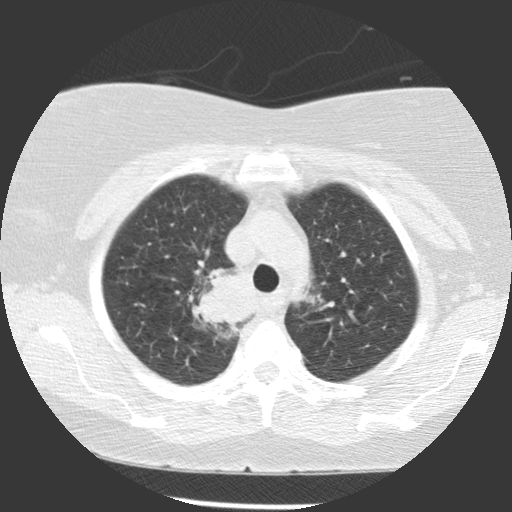
Axial slice from a low-dose chest CT screening exam; first (baseline) screen; lung window (W 1500 / L -600 HU); 2.5 mm slice thickness; standard (soft-tissue) reconstruction kernel (STANDARD); 140 kVp; slice 90 of 116 in the series. Female participant, aged 63 years at enrolment.
Expert reader's lesion annotation, bounding box (x1, y1, x2, y2) in pixels: (199, 266, 258, 328). The exam's reader record, not a measurement of the box and not confirmed to be the same lesion: non-calcified nodule or mass ≥4 mm, right upper lobe, 39 × 36 mm, spiculated (stellate) margins, soft tissue attenuation. Participant outcome: lung cancer diagnosed 72 days after this screen — non-small cell carcinoma, right upper lobe, carina, right main stem bronchus, poorly differentiated (G3), stage IIIA (AJCC 6th edition), 66 mm at pathology.